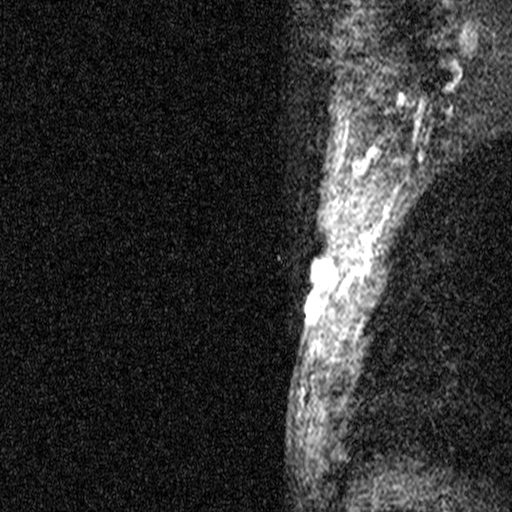
Breast MRI (dynamic contrast-enhanced), one sagittal slice. Slice 37 of 44 in the series (ordered by position). Dynamic contrast-enhanced study with each time point stored as its own series, time point 2 of 3 at this slice position (early post-contrast, ordered by acquisition time). 1.5 T. TE 4.5 ms, TR 11 ms. 3 mm slice thickness. 512 × 512 image matrix, field of view 200 × 200 mm. Female patient, age 45 years. Case-level facts recorded for this patient, not image findings: setting: breast cancer imaged before/during neoadjuvant chemotherapy; receptor status: HR-positive, HER2-negative.
Outlined on this slice (semi-automatic segmentation, software-assisted and operator-edited):
- analysis volume of interest (the breast-tissue region the enhancement analysis was run in; not a lesion): bounding box [x1, y1, x2, y2] px = [256, 218, 348, 359]
- tumour enhancement mask (voxels above the 90 % enhancement threshold inside the analysis volume of interest): [304, 262, 336, 309]